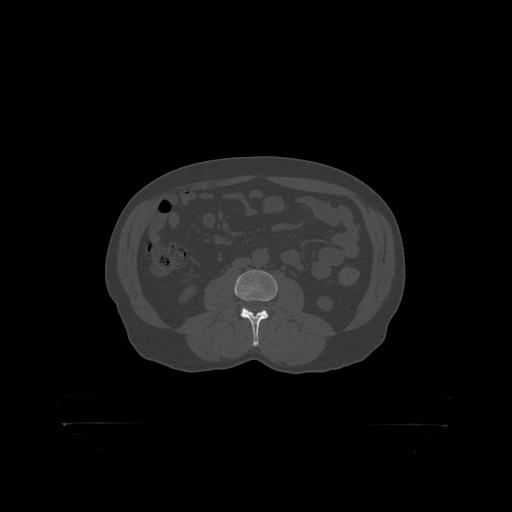
CT including the spine, one axial slice. Slice 260 of 399 in the series (ordered by position). 120 kVp. Bone window (W 1800 / L 400 HU). 1.25 mm slice thickness. 512 × 512 image matrix, field of view 650 × 650 mm. Patient: male, 46 years. From the clinical record (not read from this slice): primary cancer: skin.
Structures marked on this image (semi-automatically segmented with operator editing):
- L3 vertebra: bounding box [x1, y1, x2, y2] px = [235, 271, 278, 319]